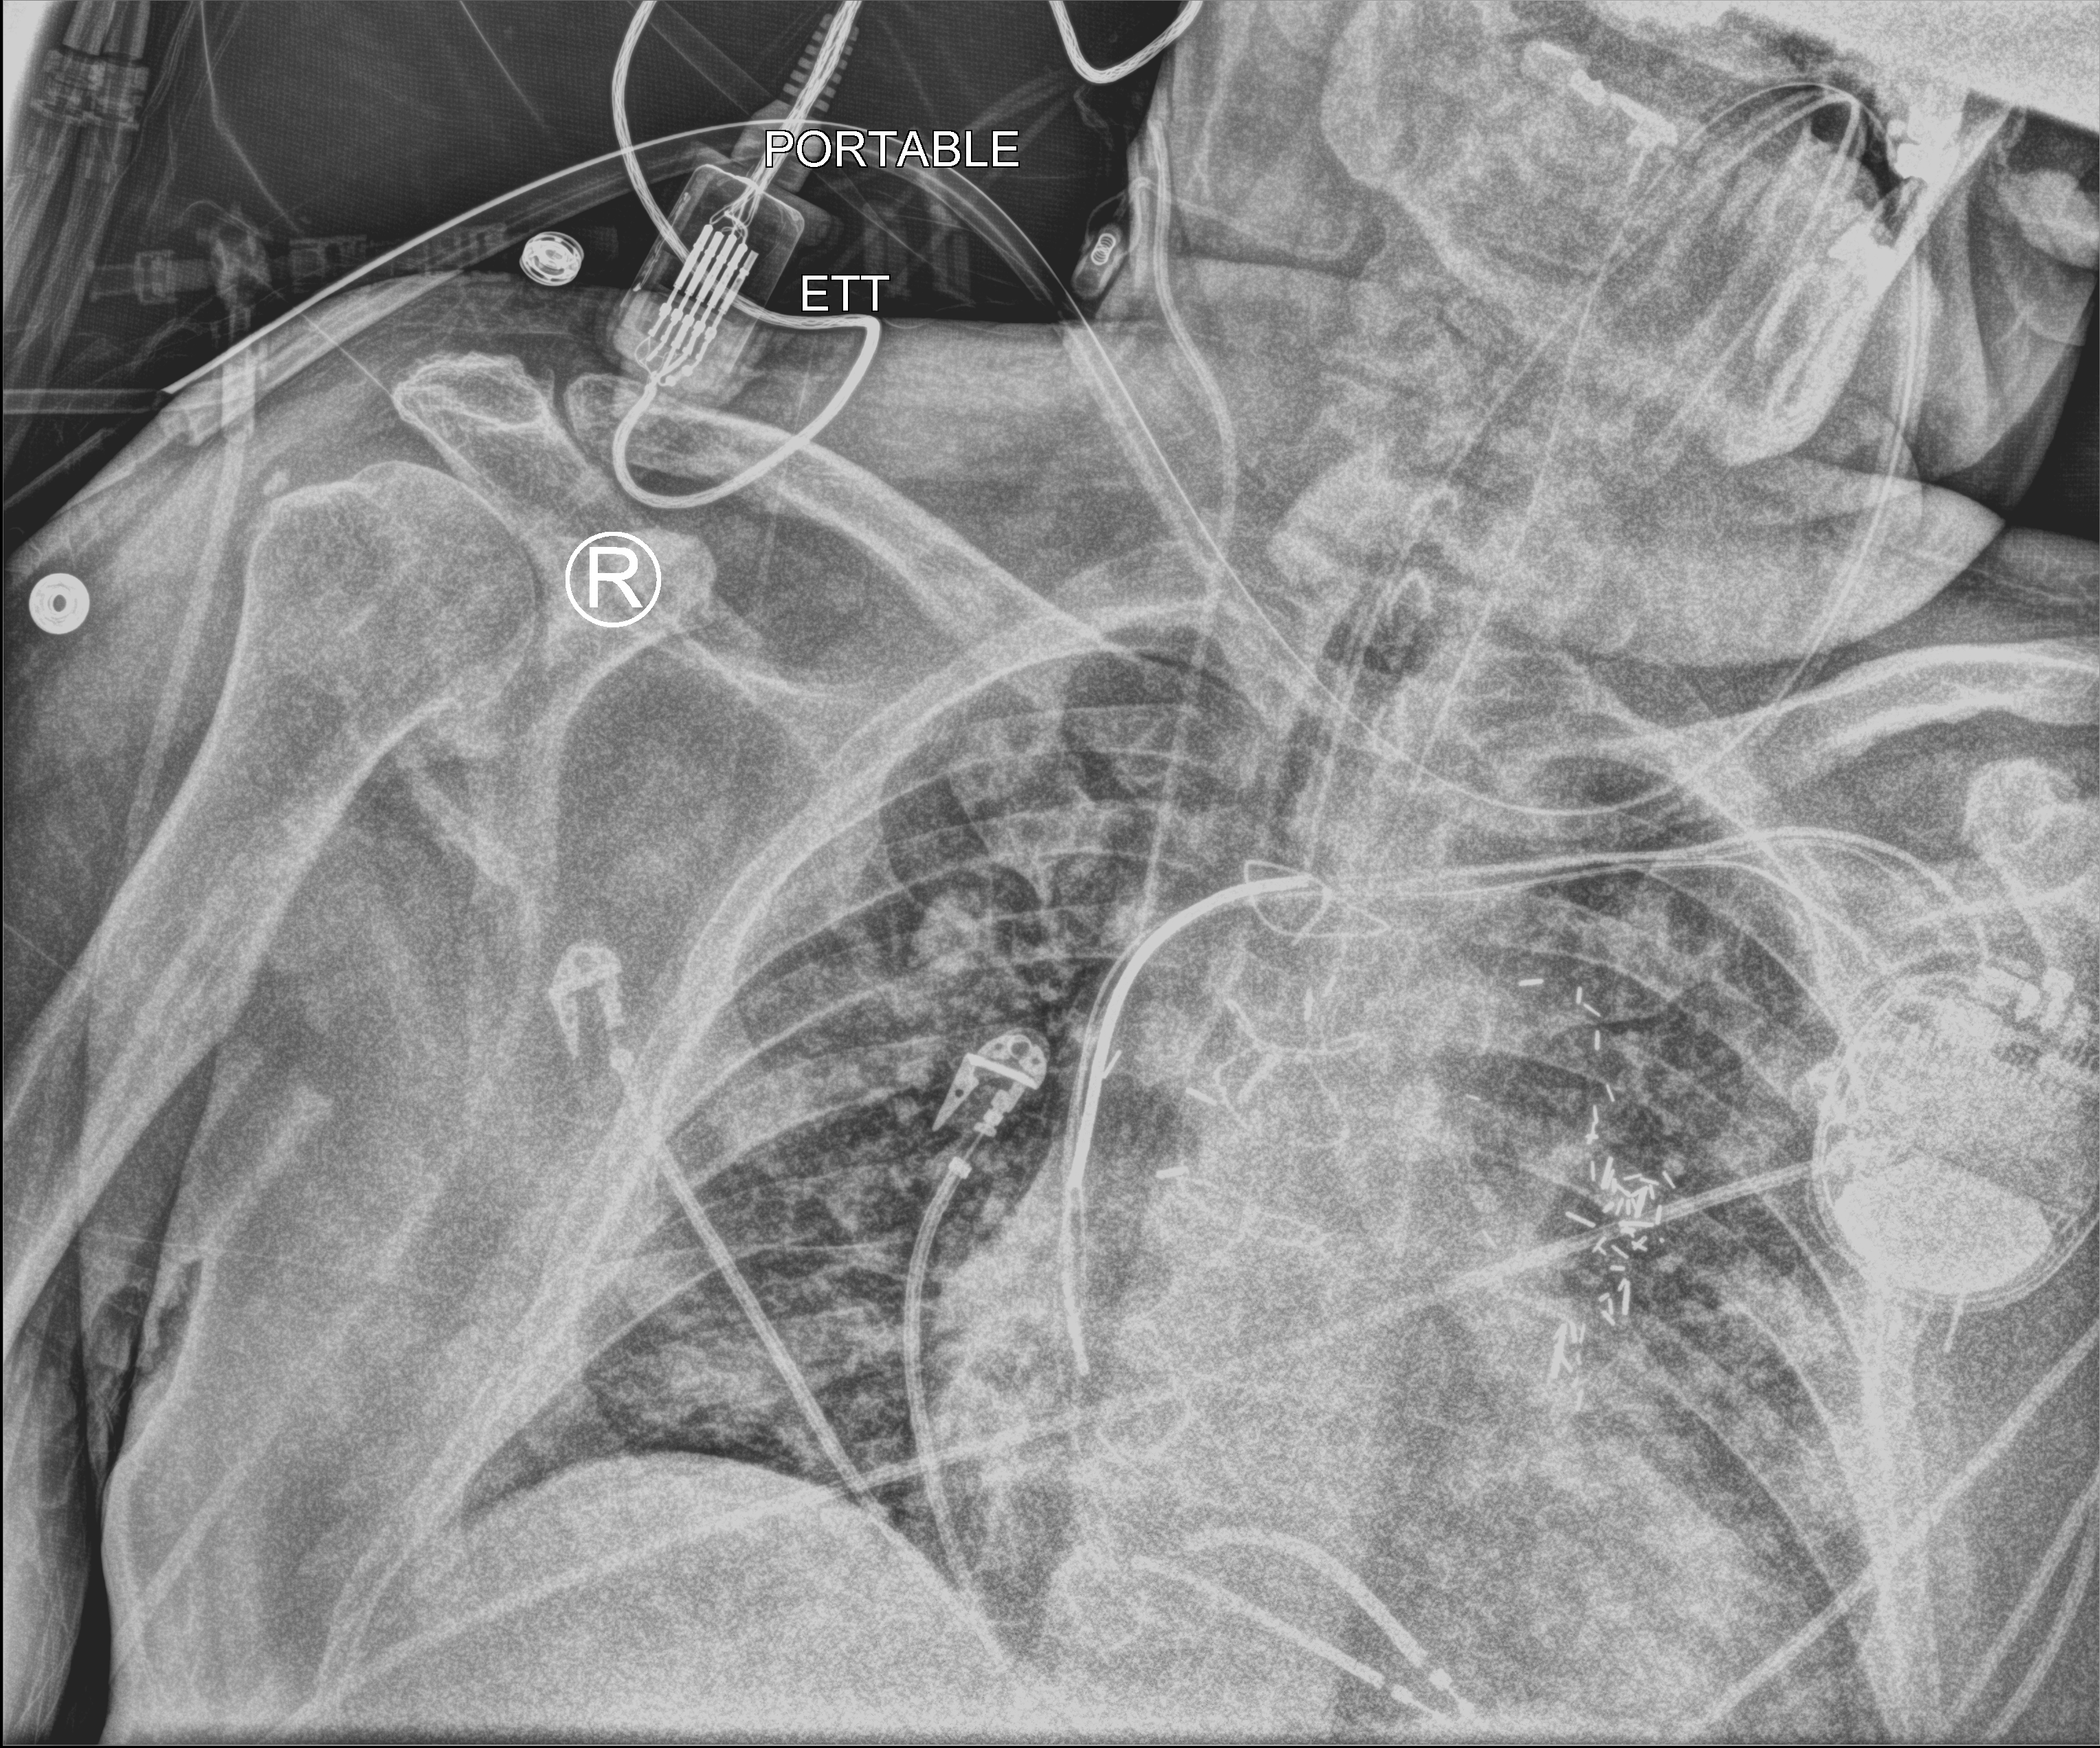
Chest X-ray (portable); anteroposterior (AP) projection. Male patient hospitalised with COVID-19, age 60–74 years.
Hospital-stay facts (about this admission, not read from this image; timing relative to this image not recorded): mechanically ventilated during this hospital stay: yes.